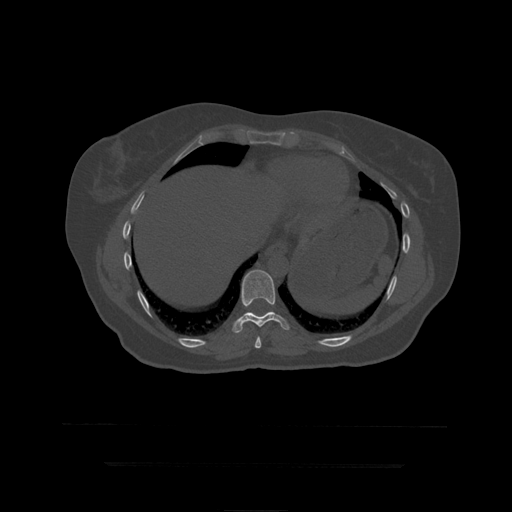
CT including the spine, one axial slice; slice 242 of 399 in the series (ordered by position); reconstruction kernel STANDARD; 120 kVp; bone window (W 1800 / L 400 HU); 1.25 mm slice thickness; 512 × 512 image matrix, field of view 450 × 450 mm. Patient age 41 years. From the clinical record (not read from this slice): primary cancer: breast.
Structures marked on this image (semi-automatically segmented with operator editing):
- T10 vertebra: bounding box (x1, y1, x2, y2) in pixels: (232, 270, 290, 334)
- T9 vertebra: (255, 336, 262, 350)